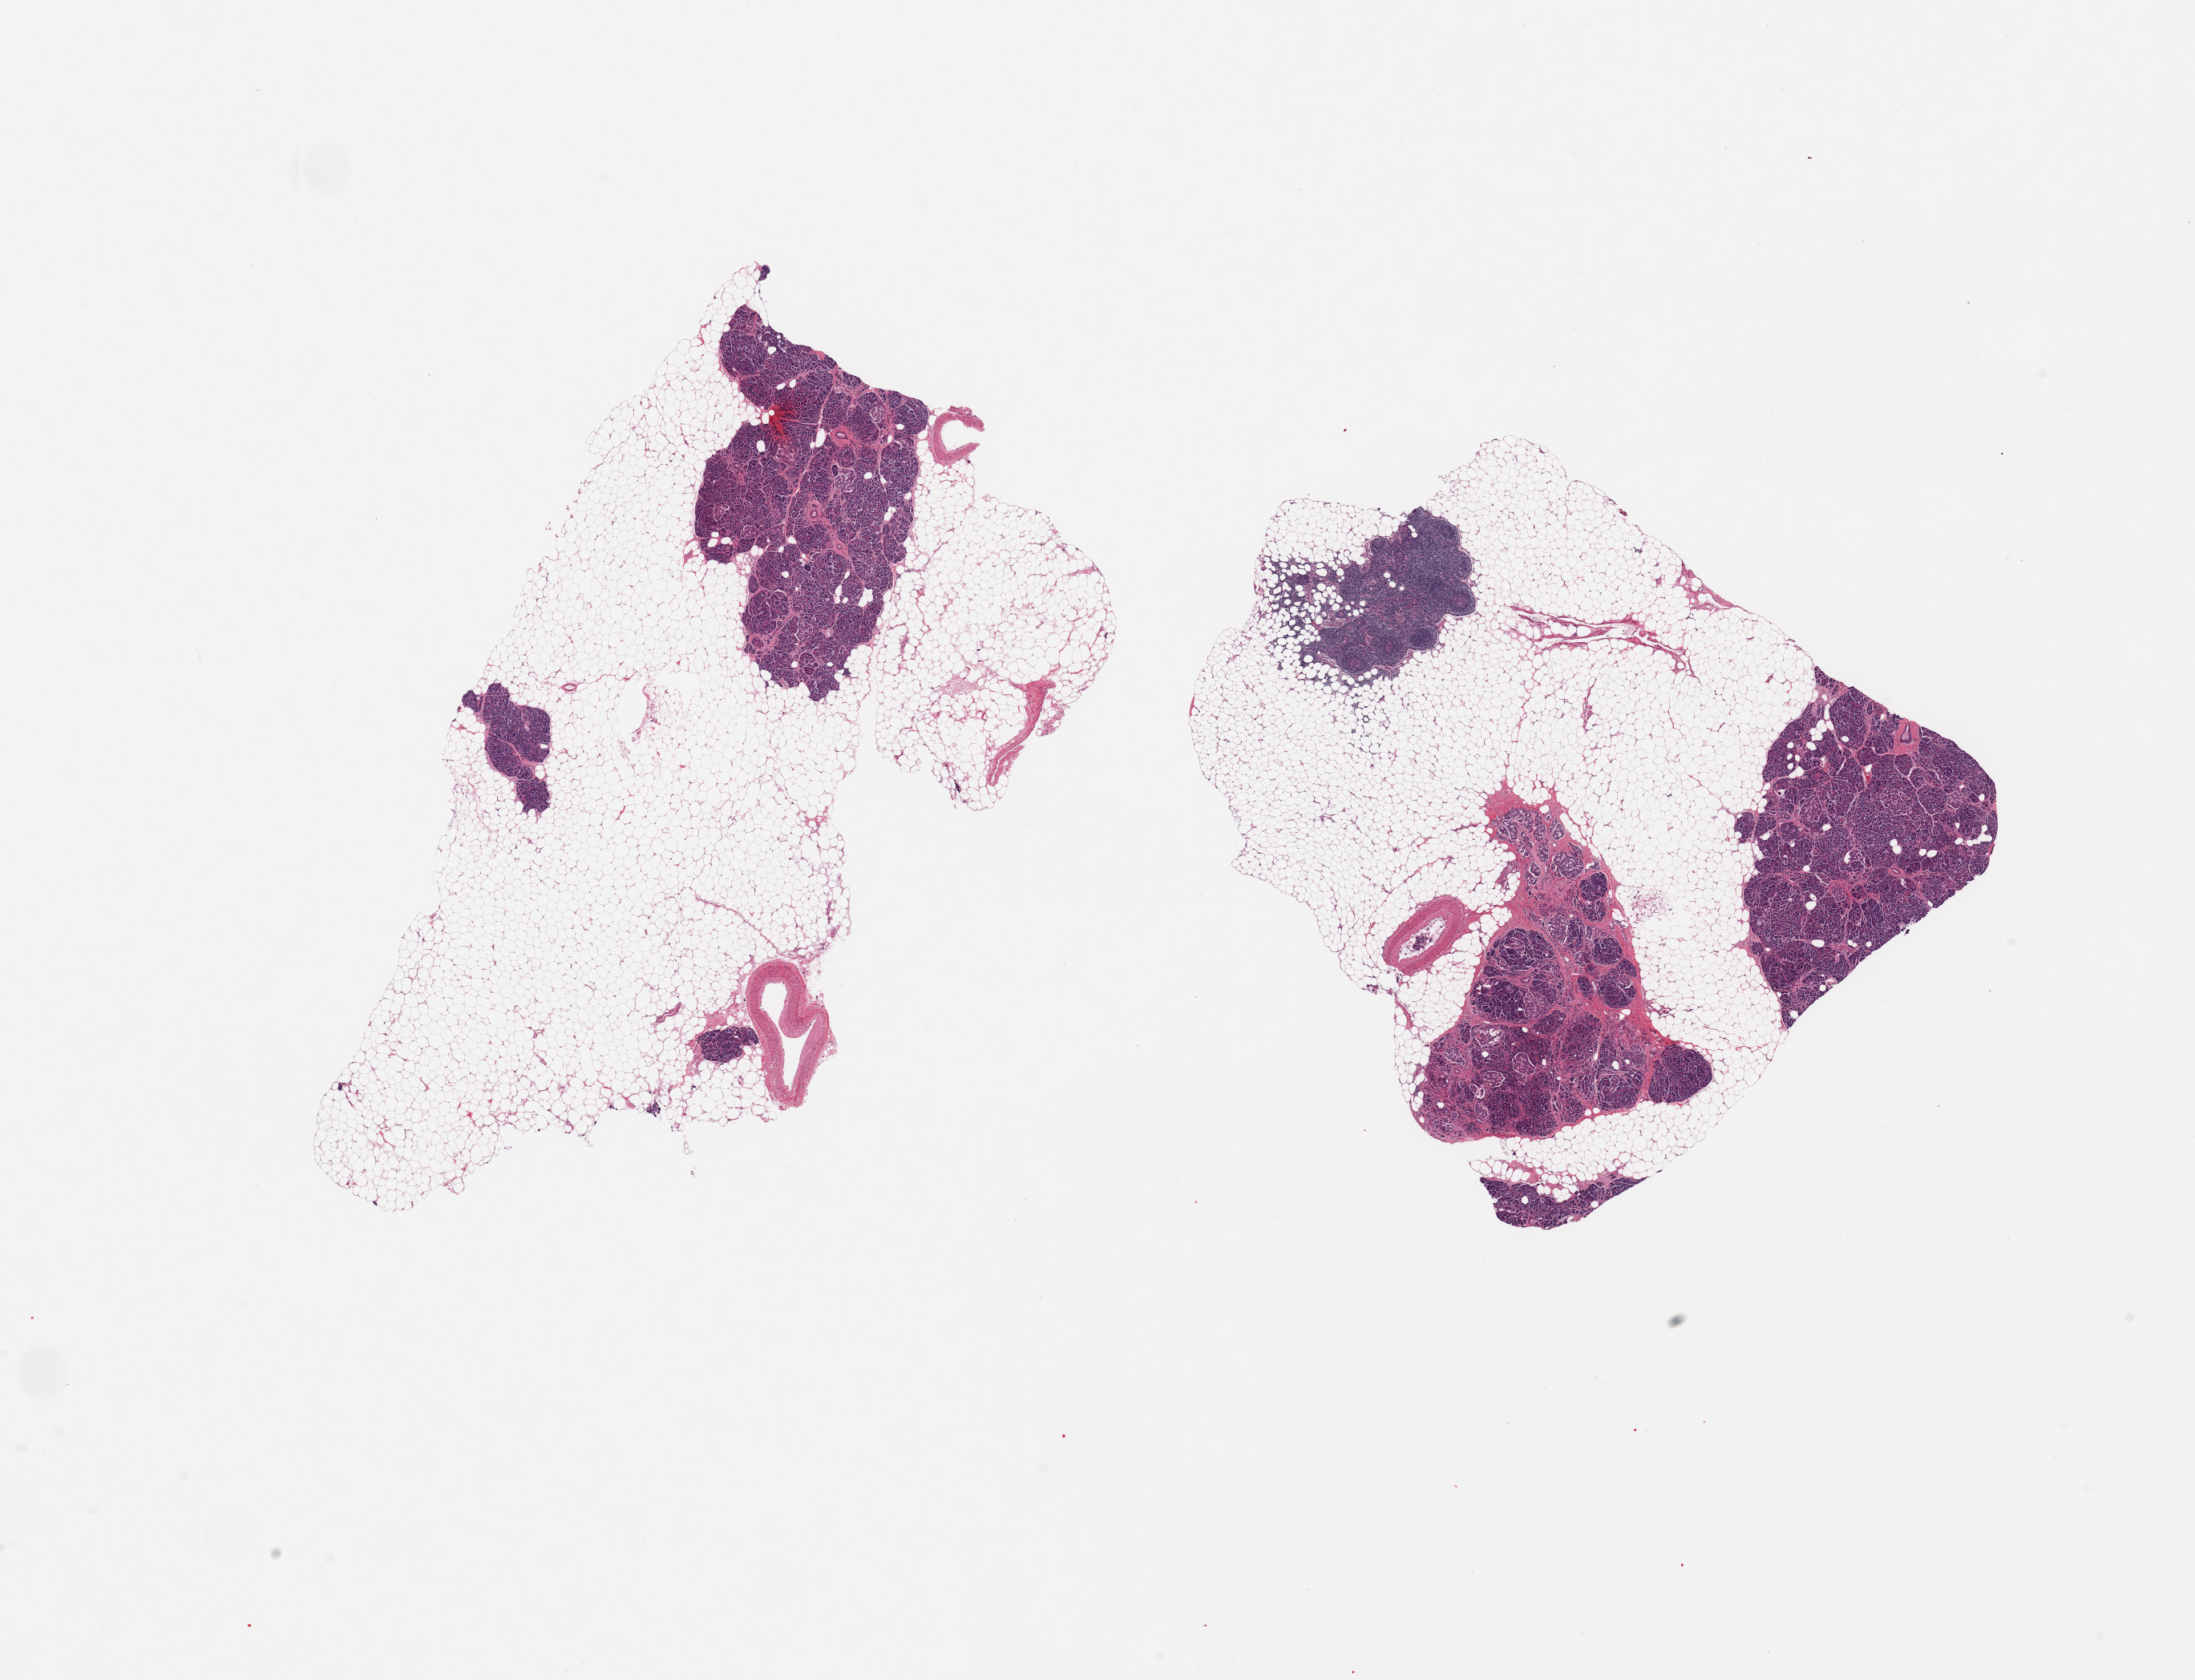
Haematoxylin and eosin whole-slide image, a low-resolution overview of the entire scanned area, about 21.7 x 16.6 mm; PAXgene-fixed paraffin-embedded (PFPE) section; sampled site (target tissue): pancreas; tissue donor sample.
- pathologist's review note for this sample: 2 pieces; largely fat and incidental lymph node with ~30% pancreatic parenchyma, some fibrosis and atrophy